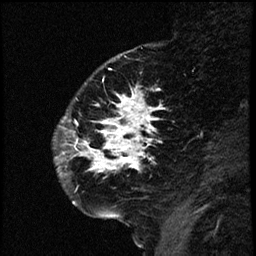
Breast MRI (dynamic contrast-enhanced), one sagittal slice; dynamic contrast-enhanced study with each time point stored as its own series, time point 2 of 3 at this slice position (early post-contrast, ordered by acquisition time); 1.5 T; TE 4.2 ms, TR 17.6 ms; 2 mm slice thickness; 256 × 256 image matrix. Female patient. From the clinical record (not read from this slice): setting: breast cancer imaged before/during neoadjuvant chemotherapy; receptor status: HER2-positive.
Annotated regions visible in this slice (semi-automatically segmented with operator editing):
- analysis volume of interest (the breast-tissue region the enhancement analysis was run in; not a lesion): bounding box (x1, y1, x2, y2) in pixels: (56, 69, 167, 209)
- tumour enhancement mask (voxels above the 100 % enhancement threshold inside the analysis volume of interest): (58, 88, 163, 176)